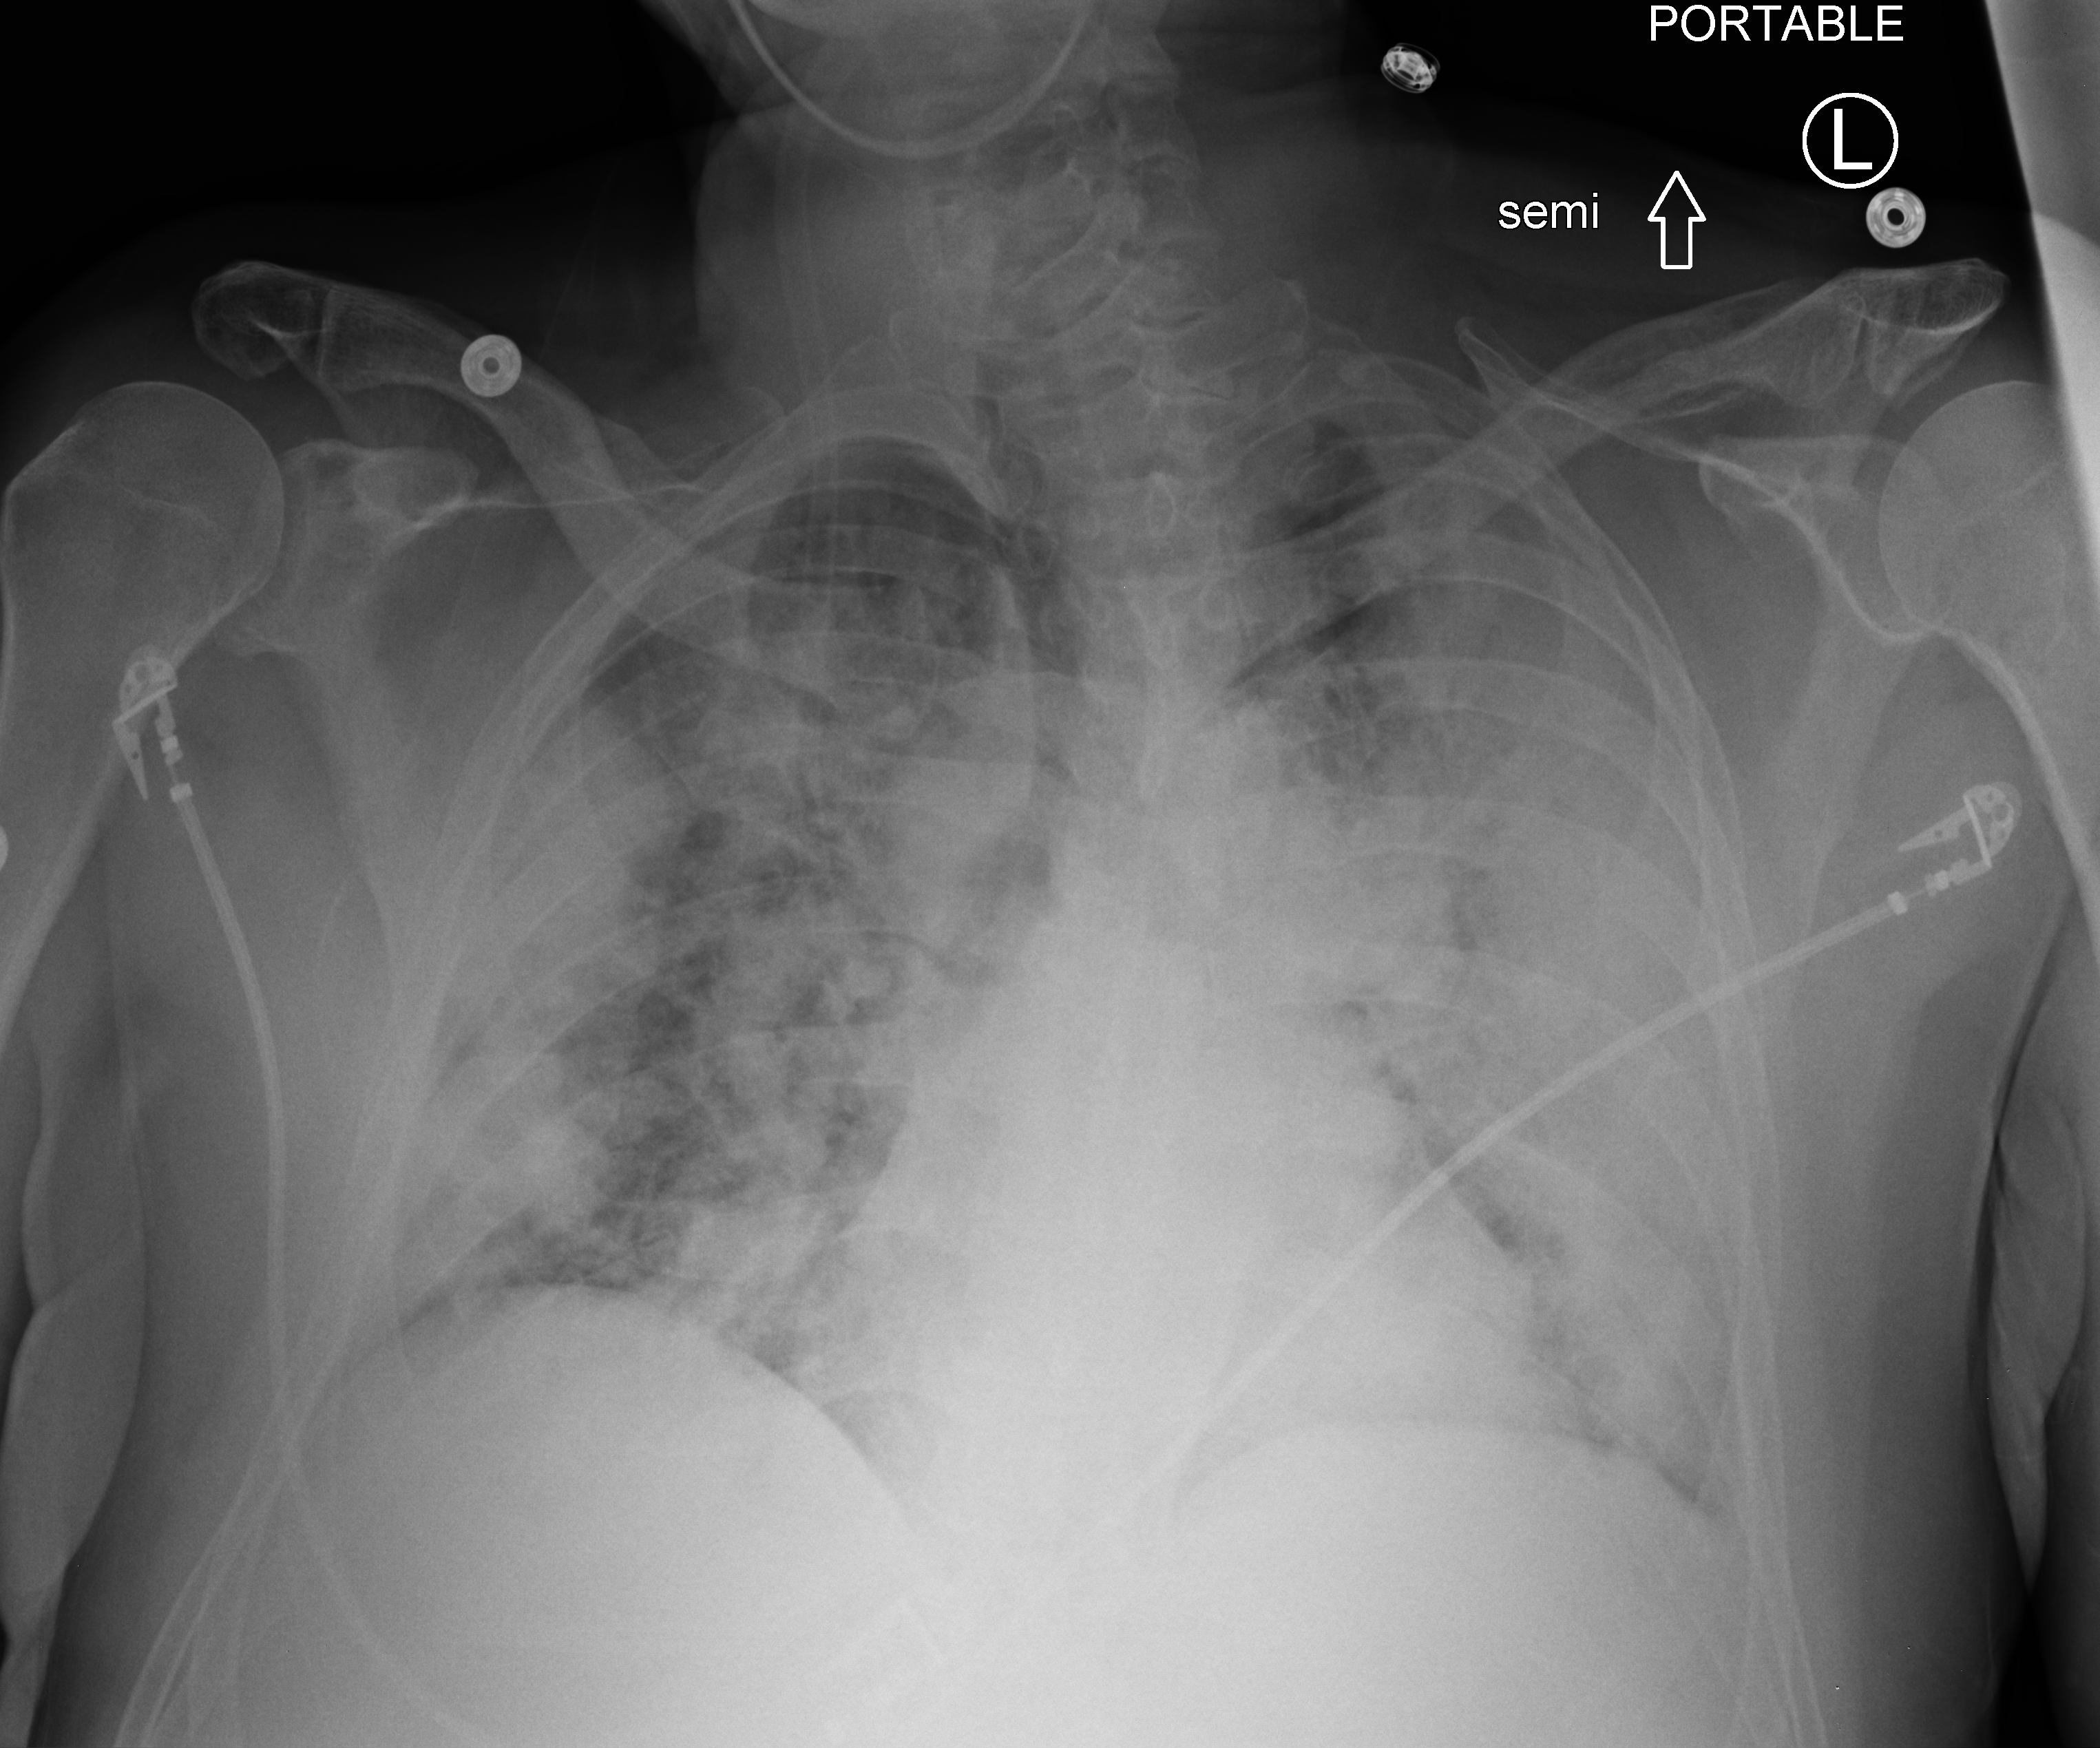
Bedside chest radiograph (computed radiography); anteroposterior (AP) projection. Patient hospitalised with COVID-19; male, aged 18–59 years.
Admission-level facts for this patient (not findings on this image; timing relative to this image not recorded): admitted to intensive care during this hospital stay: yes; length of hospital stay: 25 days.